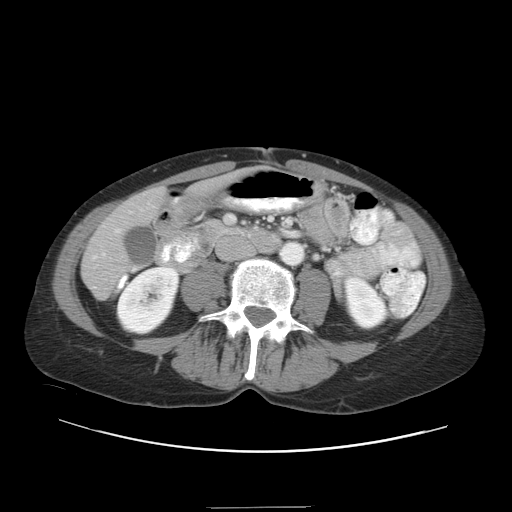
Contrast-enhanced abdominal CT, one axial slice; slice 7 of 38 in the series (ordered by position); 120 kVp; intravenous contrast given; soft-tissue window (W 400 / L 40 HU); 5 mm slice thickness; 512 × 512 image matrix. Female patient, age 64 years. From the clinical record (not read from this slice): diagnosis: colorectal cancer liver metastases, imaged before liver resection; multiple liver metastases: no; largest metastasis: 3.8 cm; chemotherapy before resection: yes.
Outlined on this slice (expert manual segmentation):
- hepatic veins: bounding box <115,229,120,233> (left, top, right, bottom; pixels)
- liver: <84,192,162,297>
- planned liver remnant (the part of the liver to remain after resection): <204,185,213,188>